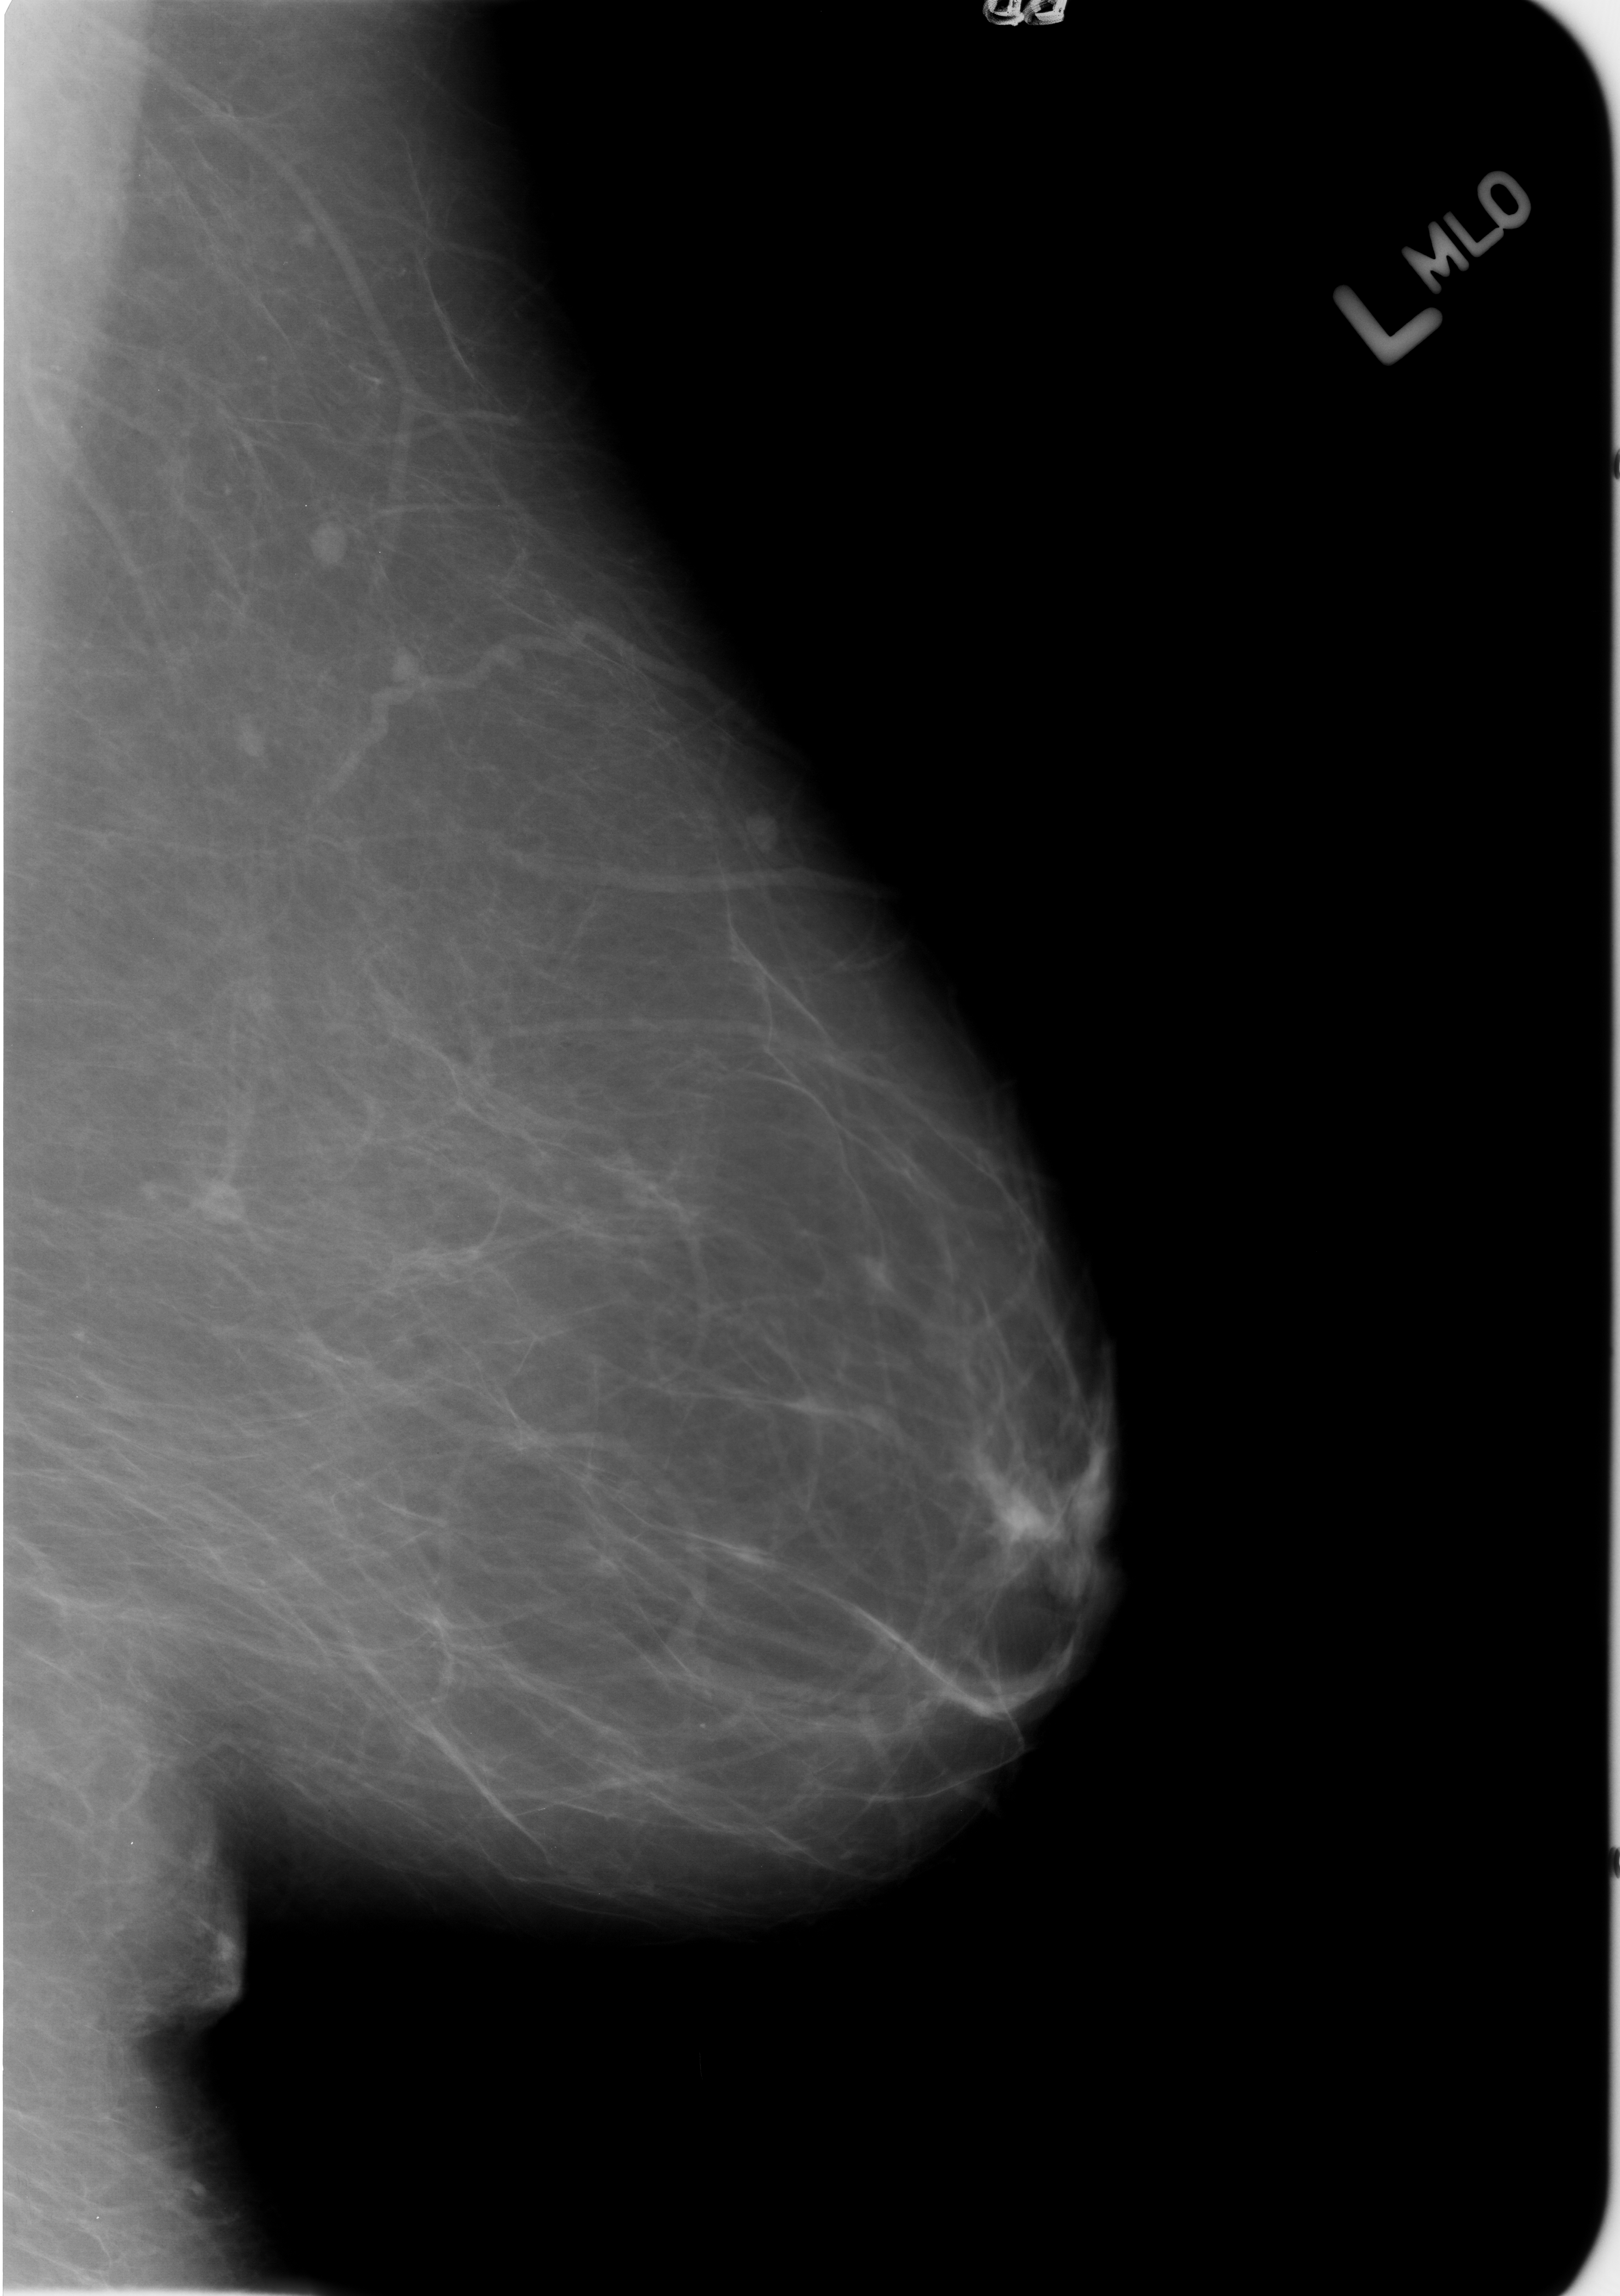
Scanned film-screen mammogram; left breast; MLO view; BI-RADS breast density category 1 (scale 1–4); 1620 × 2296 image matrix.
Expert-marked regions of interest on this image (one box per marked abnormality):
- Finding 1 of 5: mass, shape lymph node, margins circumscribed; BI-RADS assessment category 2; subtlety rating 4 on a 1 (subtle) to 5 (obvious) scale; benign; no additional work-up was recommended (outcome (as recorded, no biopsy): benign without callback): bounding box (x1, y1, x2, y2) in pixels: (183, 1176, 264, 1243)
- Finding 2 of 5: mass, shape lymph node, margins circumscribed; BI-RADS assessment category 2; outcome (as recorded, no biopsy): benign without callback (not worked up further): (225, 707, 271, 773)
- Finding 3 of 5: mass, shape lymph node, margins circumscribed; BI-RADS assessment category 2; subtlety rating 4 on a 1 (subtle) to 5 (obvious) scale; benign; no additional work-up was recommended (outcome (as recorded, no biopsy): benign without callback): (298, 509, 356, 579)
- Finding 4 of 5: mass, shape lymph node, margins circumscribed; BI-RADS assessment category 2; subtlety rating 4 on a 1 (subtle) to 5 (obvious) scale; benign; no additional work-up was recommended (outcome (as recorded, no biopsy): benign without callback): (368, 639, 438, 702)
- Finding 5 of 5: mass, shape lymph node, margins circumscribed; BI-RADS assessment category 2; subtlety rating 4 on a 1 (subtle) to 5 (obvious) scale; benign; no additional work-up was recommended (outcome (as recorded, no biopsy): benign without callback): (737, 803, 794, 861)